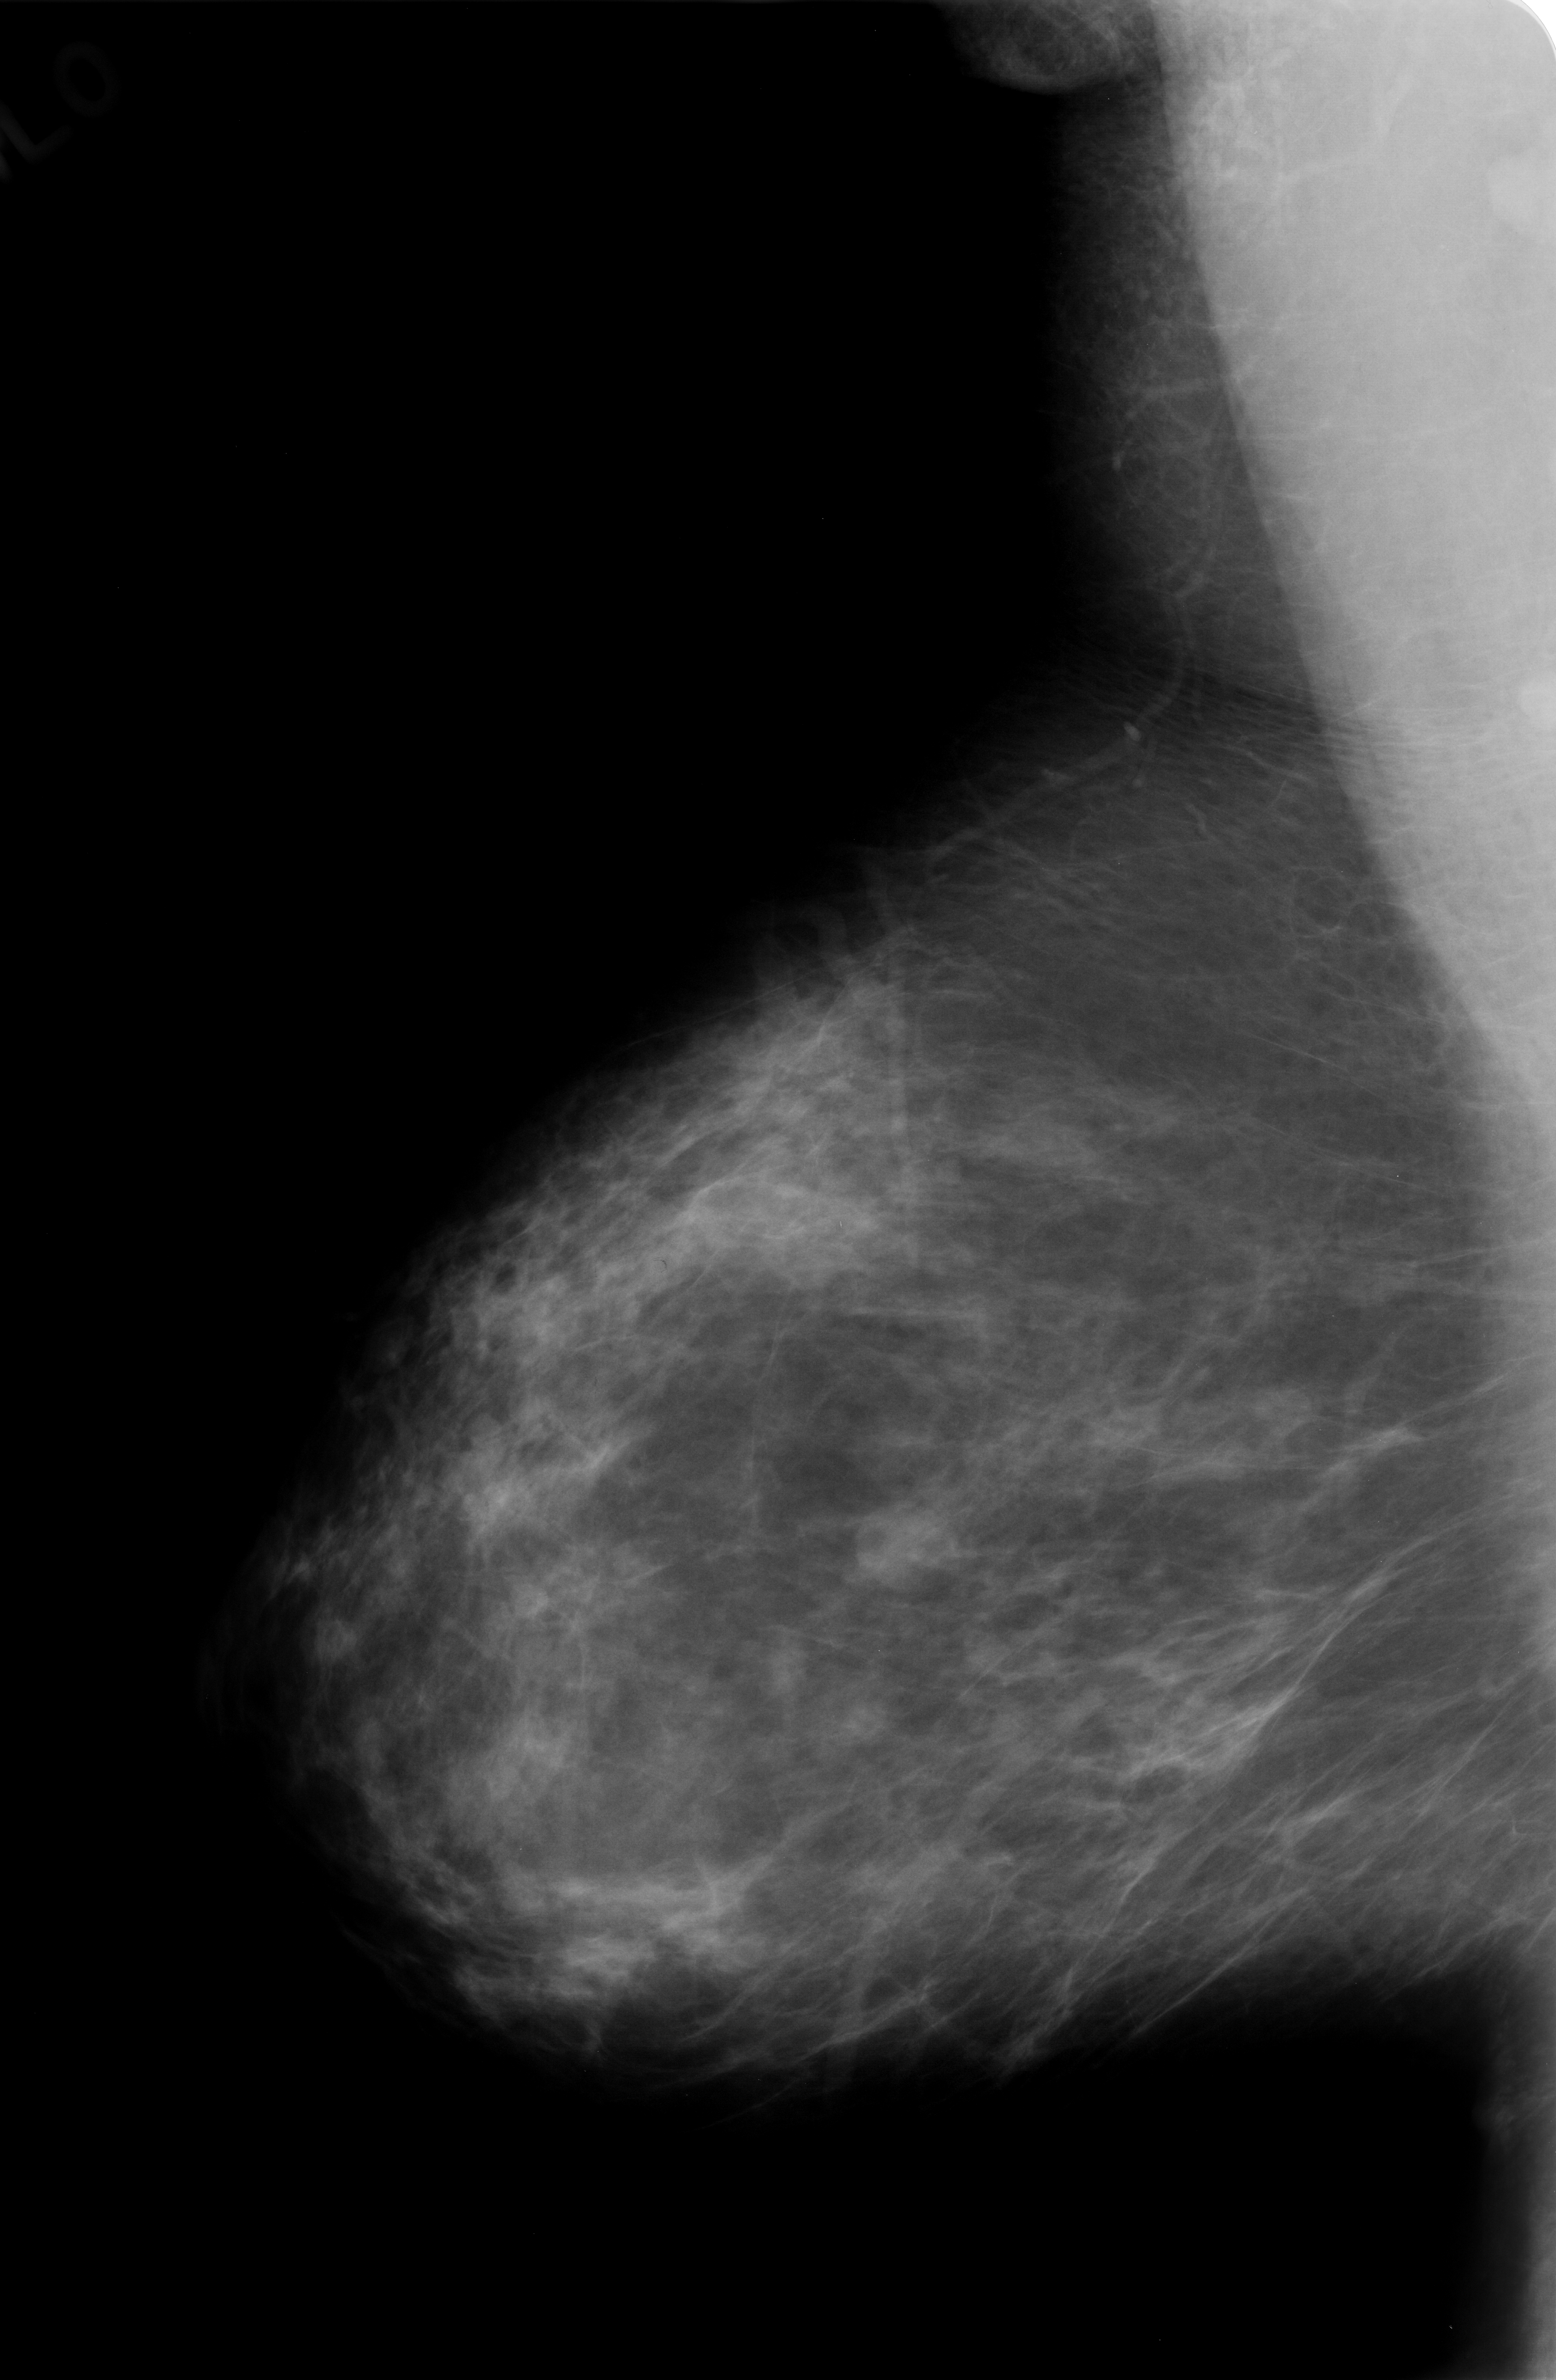
Digitized screen-film mammogram, right breast, mediolateral oblique (MLO) view.
Abnormality record for this image: mass, shape oval, margins circumscribed; BI-RADS assessment category 3; subtlety rating 4 on a 1 (subtle) to 5 (obvious) scale; pathology (as recorded): benign.